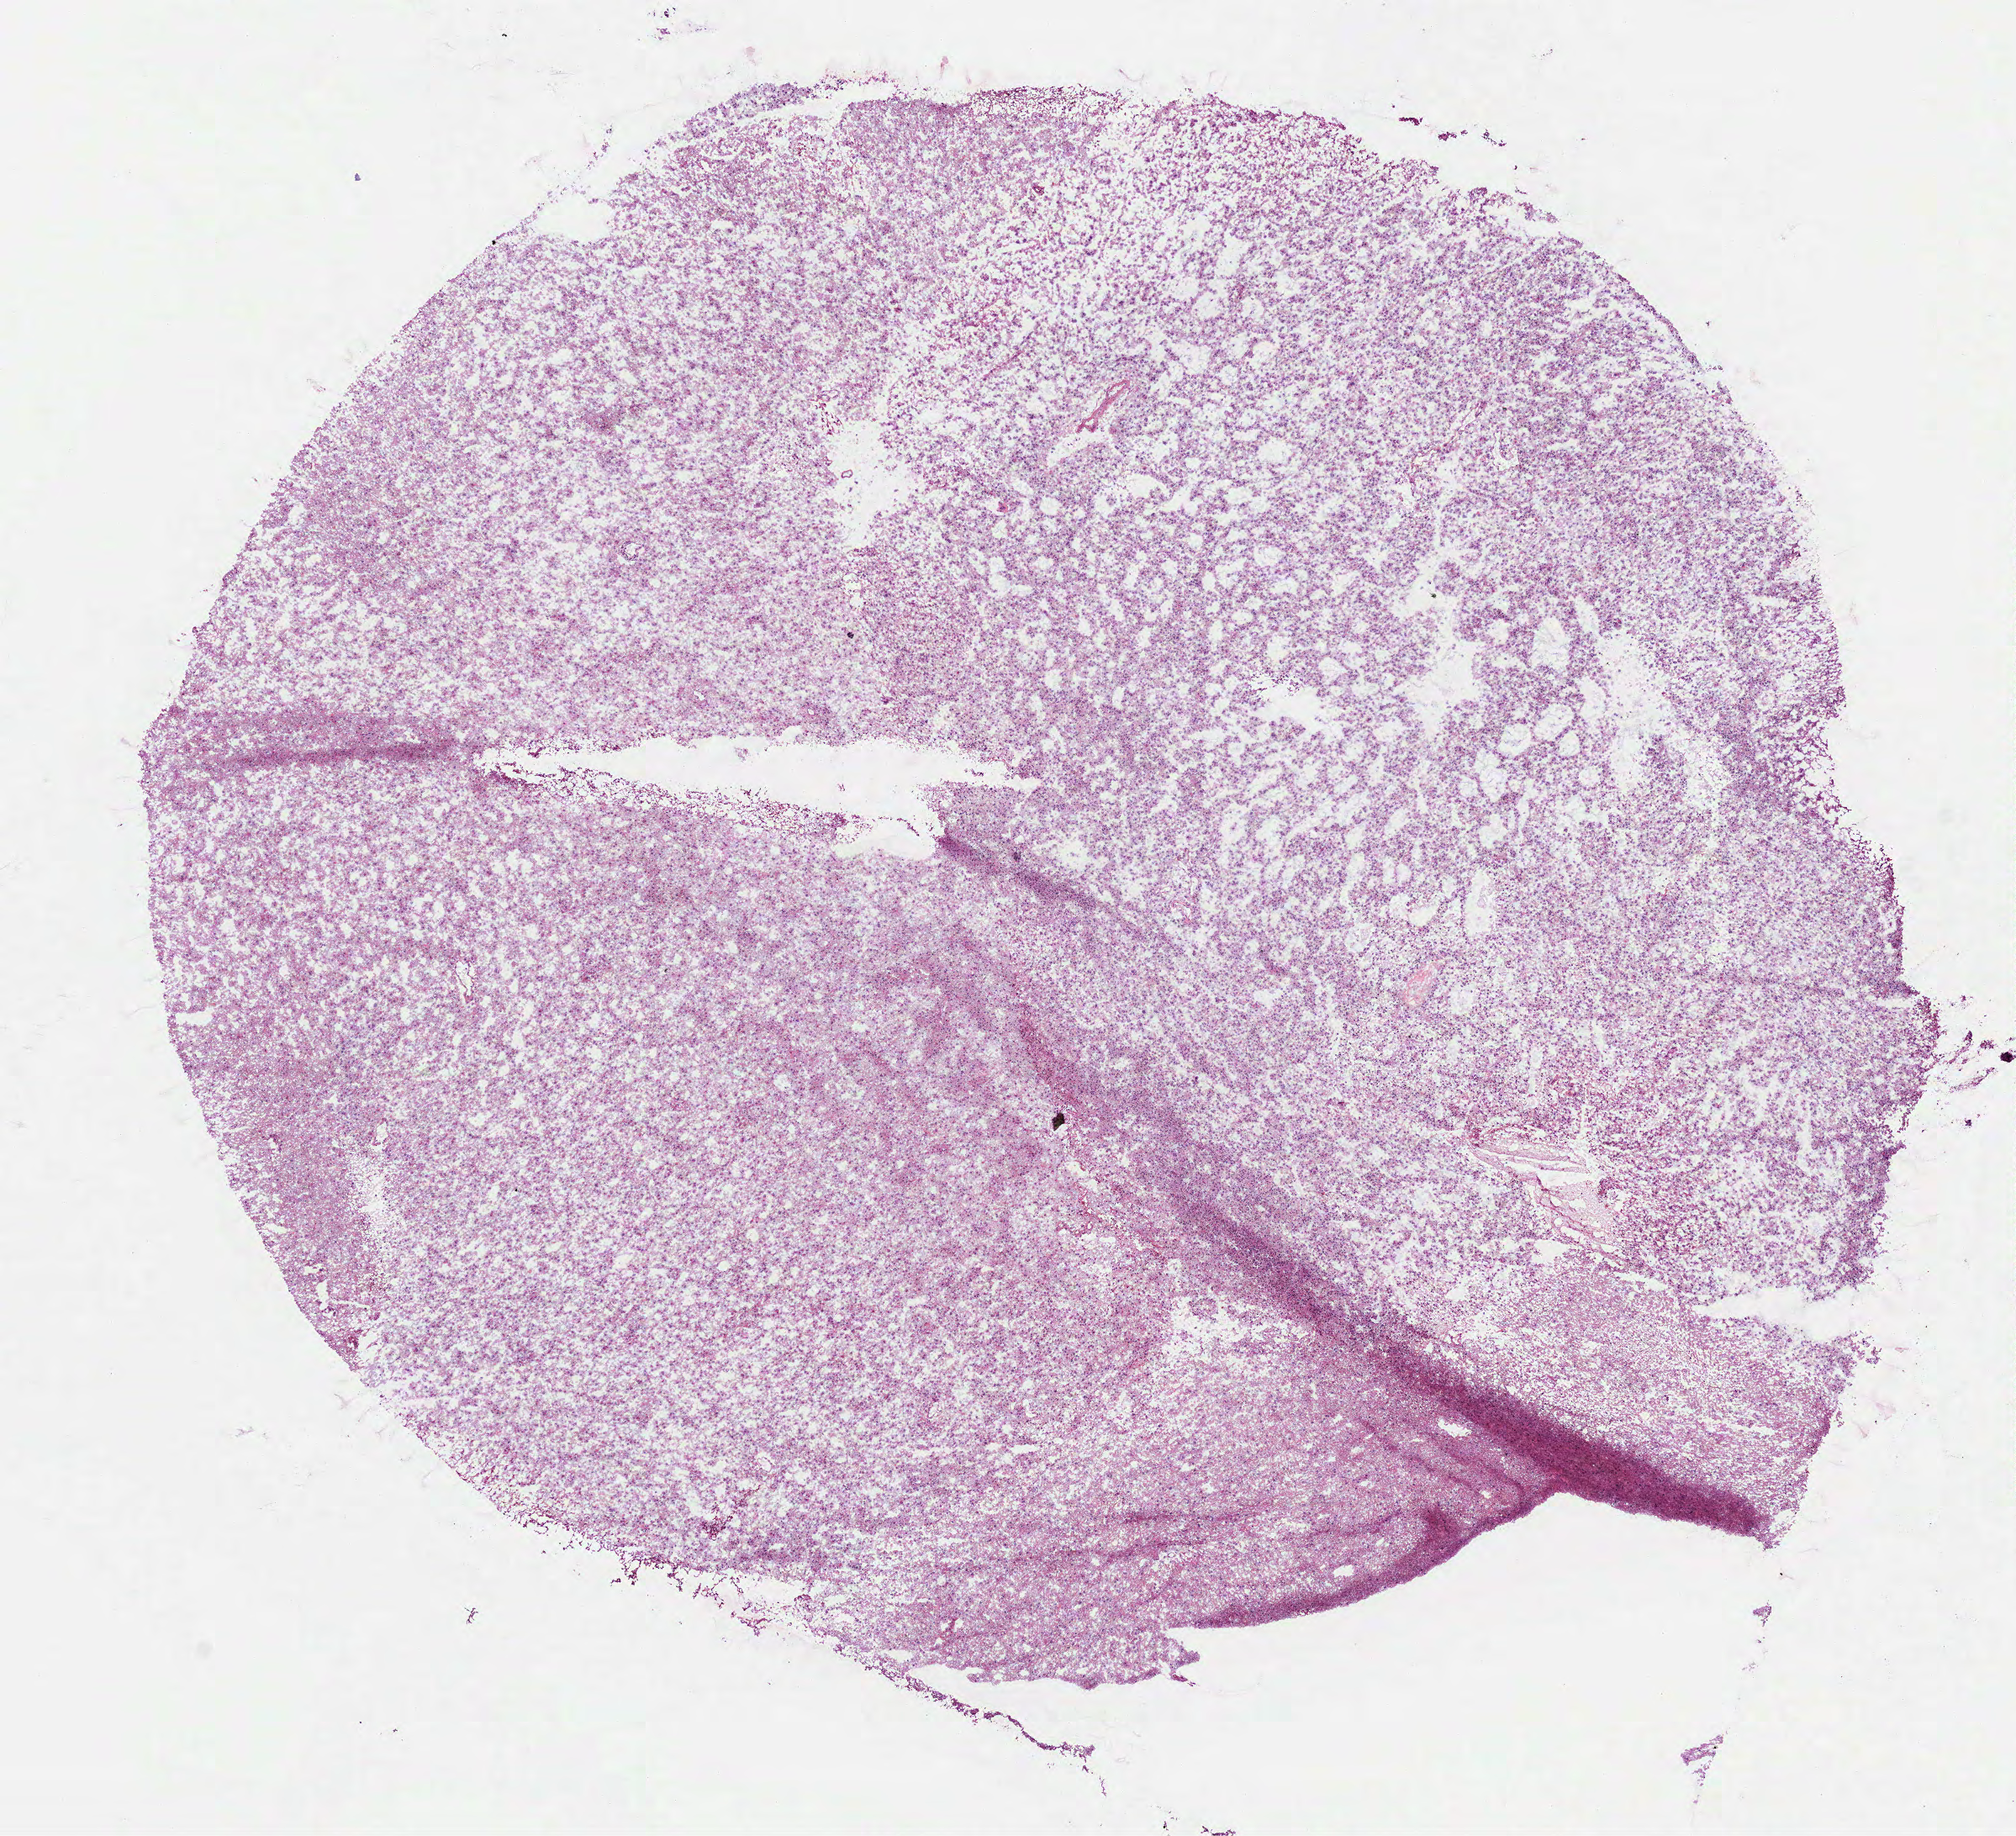
Hematoxylin and eosin (H&E) stained whole-slide image — whole scanned area (about 9.7 x 8.8 mm) shown as a low-resolution overview, frozen section from the bottom of the tissue portion, sample: primary tumour, brain. Patient: male, age at initial diagnosis 53 years. Histologic grade: G2 (moderately differentiated). Pathologist review of this section (percent, as recorded): tumour cells 100%, tumour nuclei 80%, normal cells 0%, stromal cells 0%, necrosis 0%.
Laterality: left. Diagnosis: Oligodendroglioma, NOS (cerebrum).